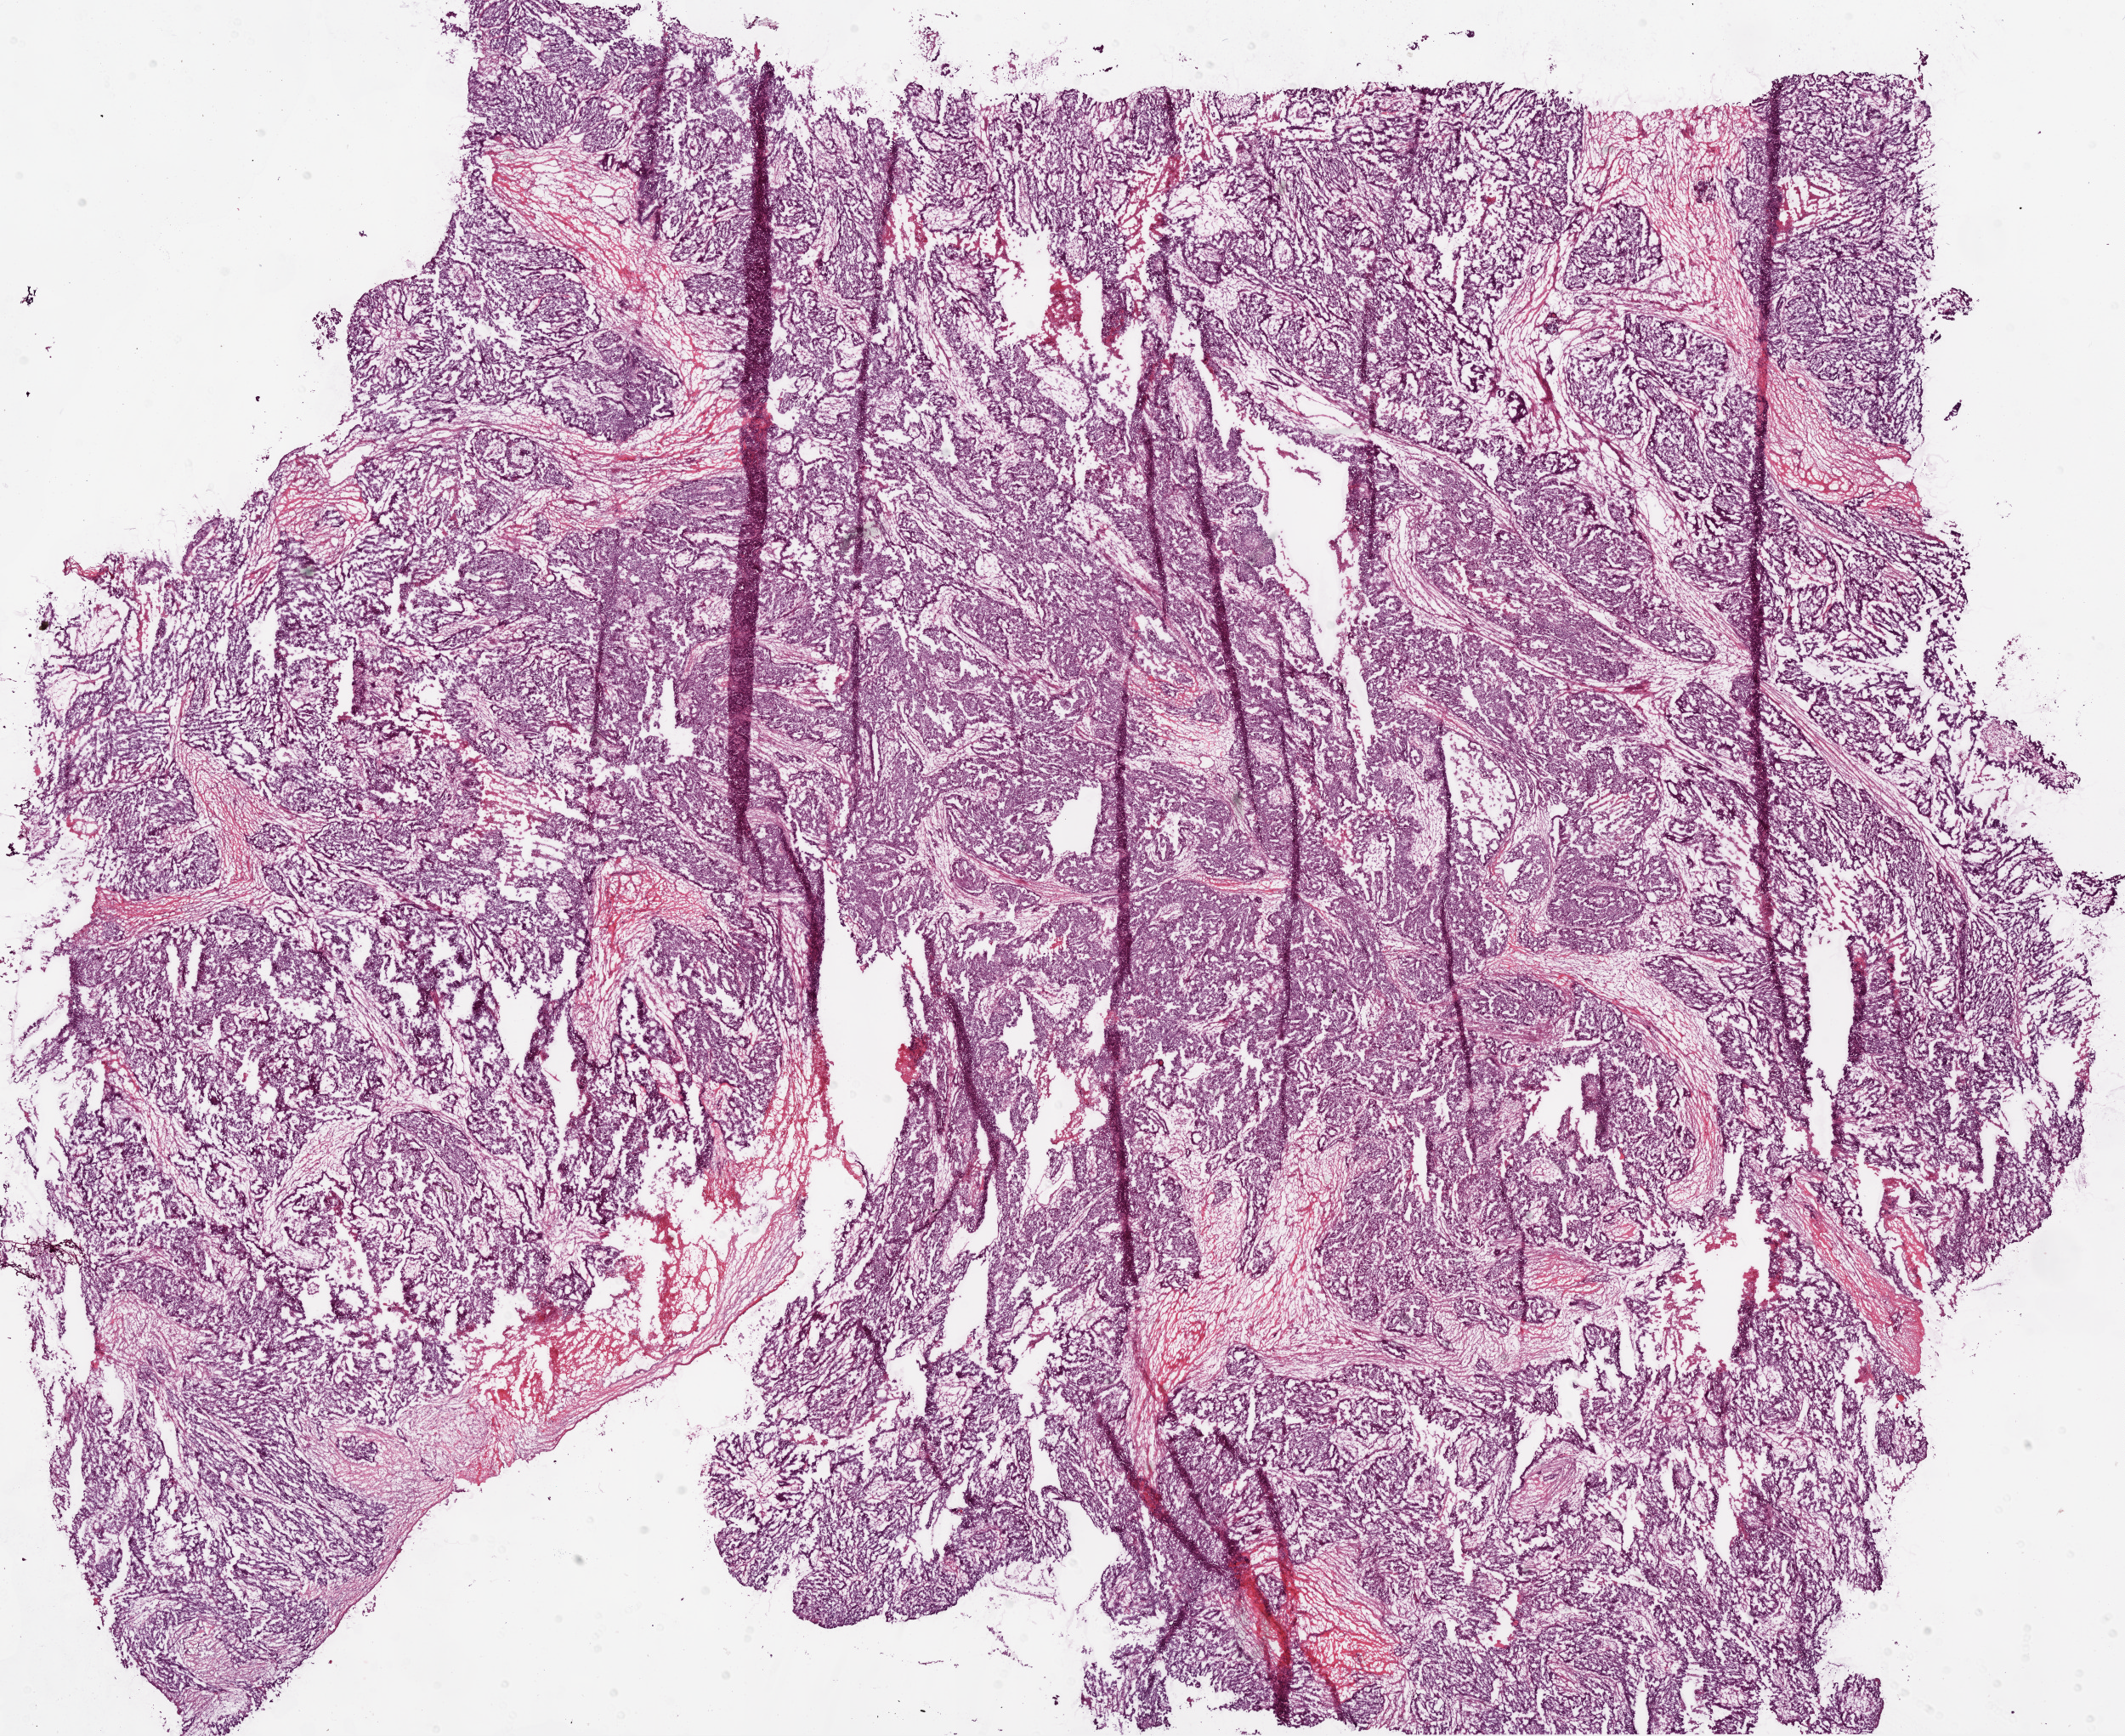
H&E-stained whole-slide image, shown as a low-resolution overview of the whole scanned area (about 20.1 x 16.4 mm, slide scanned at 20x), frozen section from the bottom of the tissue portion, sample: primary tumour, ovary. Patient: female, age at initial diagnosis 52 years. Histologic grade: G3 (poorly differentiated). Composition of this section per pathologist review: tumour cells 90%, tumour nuclei 95%, normal cells 0%, stromal cells 5%, necrosis 5%.
• diagnosis: Serous cystadenocarcinoma, NOS
• FIGO stage: IV